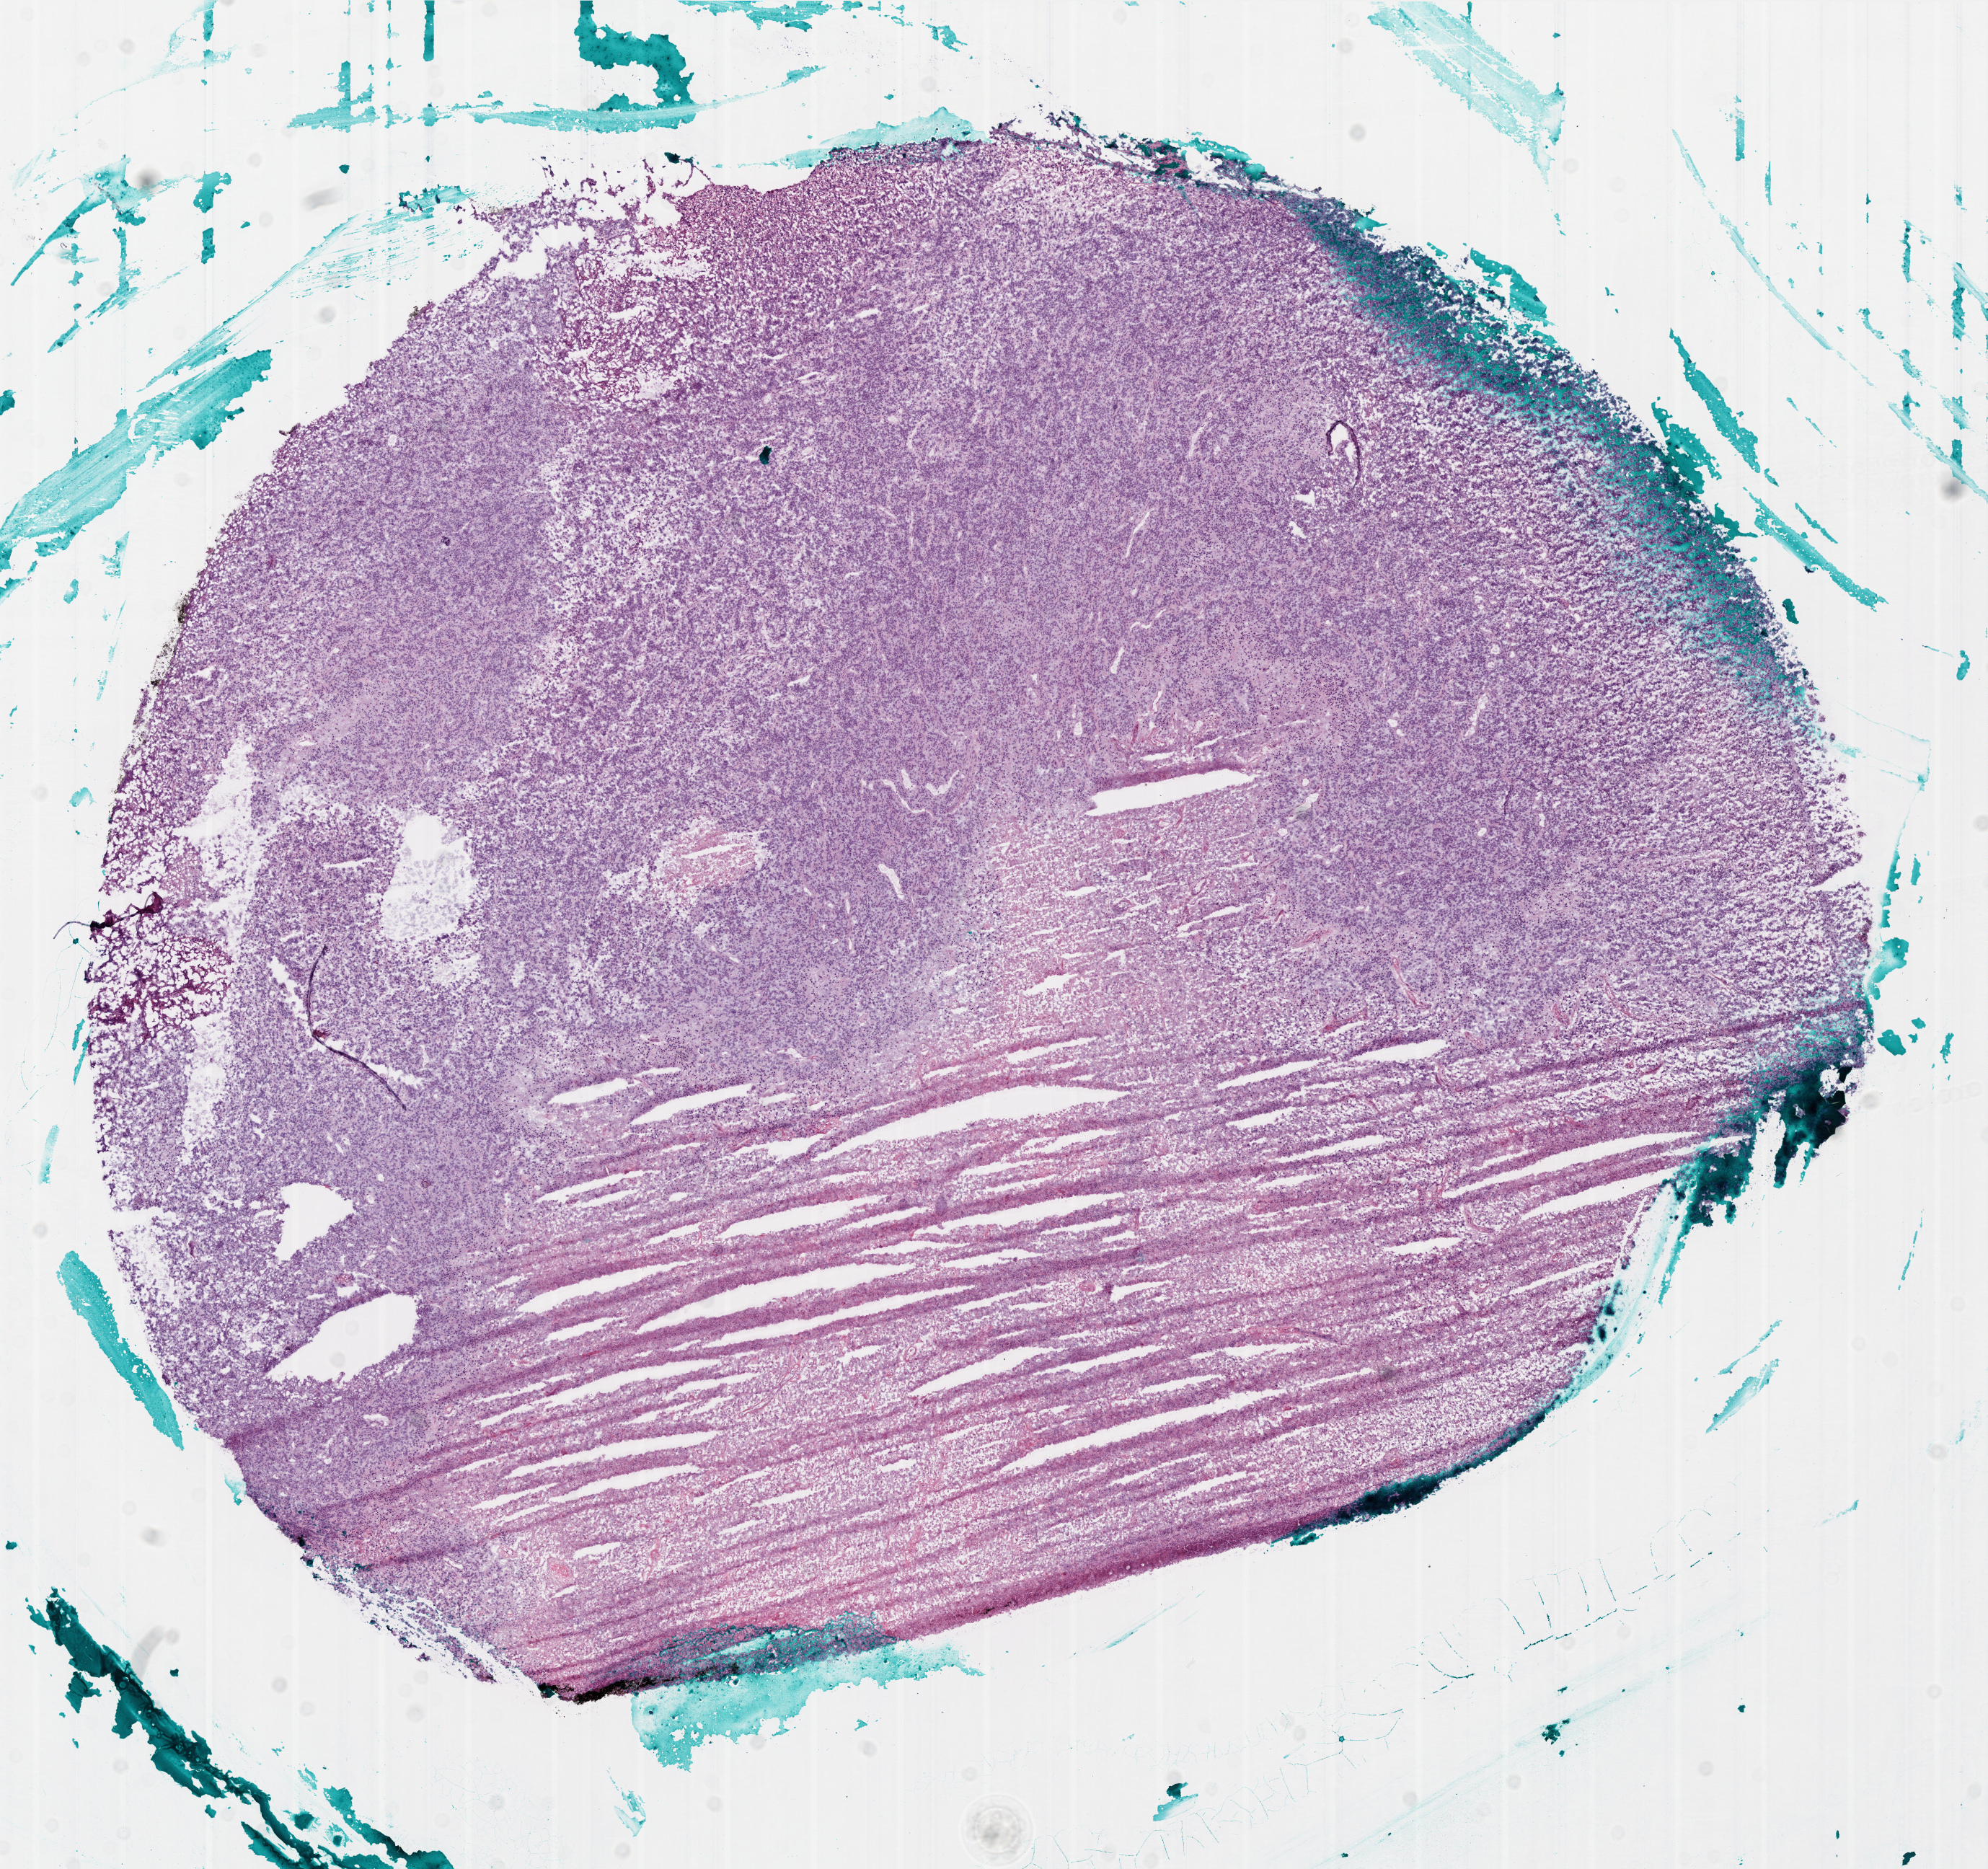
Whole-slide histology image, H&E-stained — a low-resolution overview of the entire scanned area, about 11.1 x 10.4 mm. Frozen section. Primary tumour sample from the brain. Patient: male, age at initial diagnosis 68 years. Slide review estimates, as recorded: tumour cells 59%, tumour nuclei 99%, normal cells 0%, stromal cells 0%, necrosis 41%.
• pathologic diagnosis: Glioblastoma